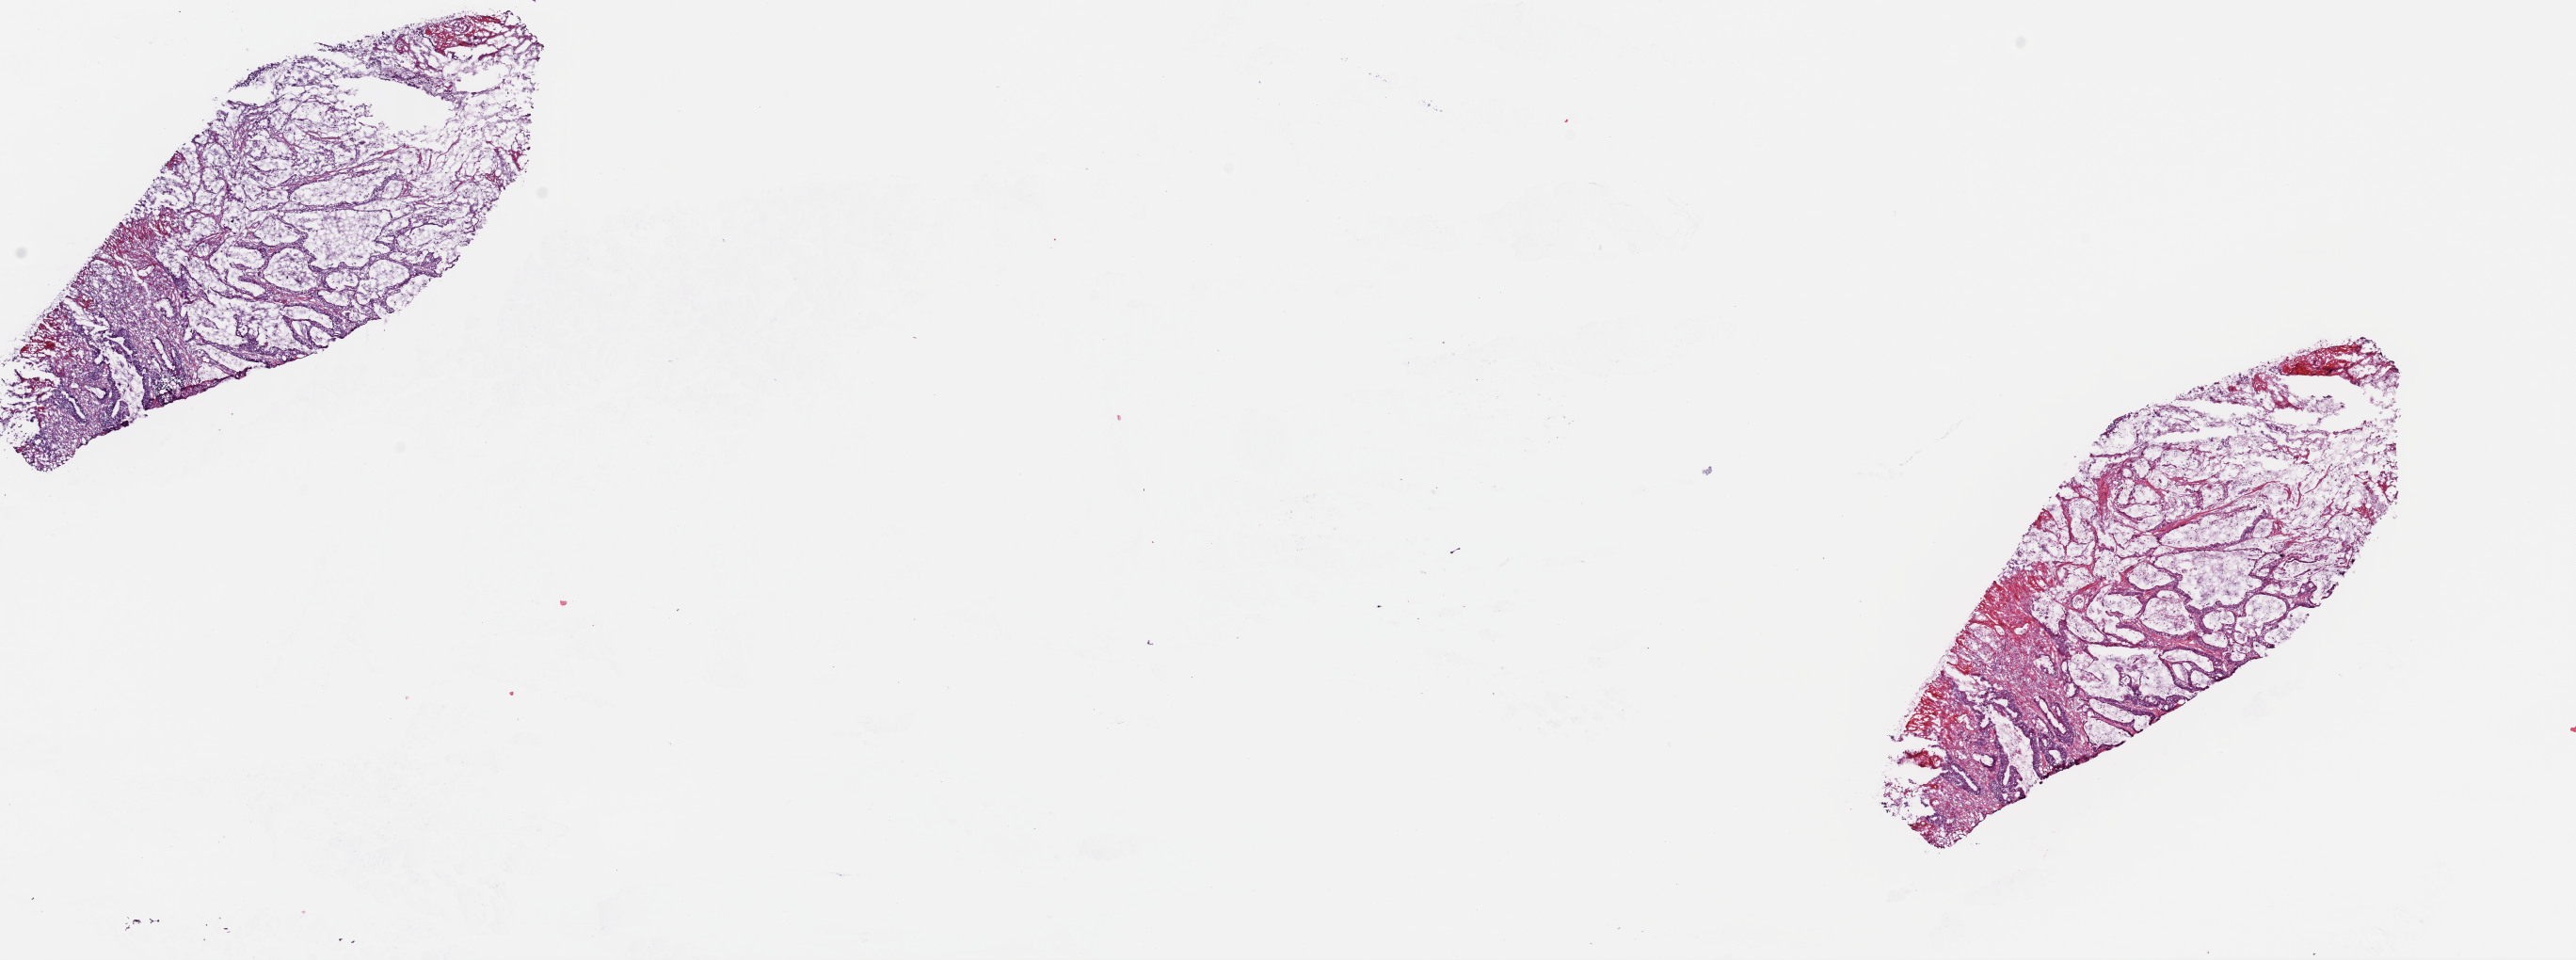
Whole-slide histology image, H&E — shown as a low-resolution overview of the whole scanned area (about 21.6 x 8.1 mm, acquisition: 40x scan); frozen section from the top of the tissue portion; colon, primary tumour sample. Female patient; age at initial diagnosis 70 years. Pathologist review of this section (percent, as recorded): tumour cells 70%, tumour nuclei 75%, normal cells 0%, stromal cells 30%, necrosis 0%. Inflammatory infiltration, as recorded: lymphocyte infiltration 1%, monocyte infiltration 1%, neutrophil infiltration 0%.
- pathologic diagnosis: Mucinous adenocarcinoma (ascending colon)
- AJCC pathologic stage: IIA (6th edition)